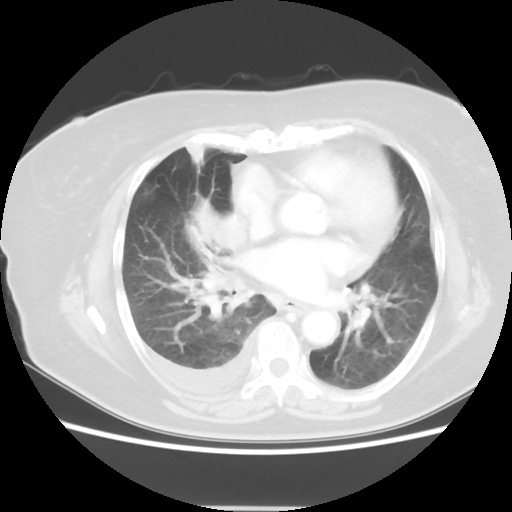
Chest CT, one axial slice; position 24 of 48 along the scan axis; 120 kVp; lung window (W 1500 / L -600 HU); 512 × 512 image matrix, field of view 360 × 360 mm. Patient: female, 73 years. From the clinical record (not read from this slice): clinical TNM (as recorded): T3 N3 M1b; histopathological grade: G3.
Structures marked on this image (rectangle marked by the reading radiologist):
- lung tumour (recorded histology: small cell carcinoma): box from (x=187, y=204) to (x=275, y=289) px